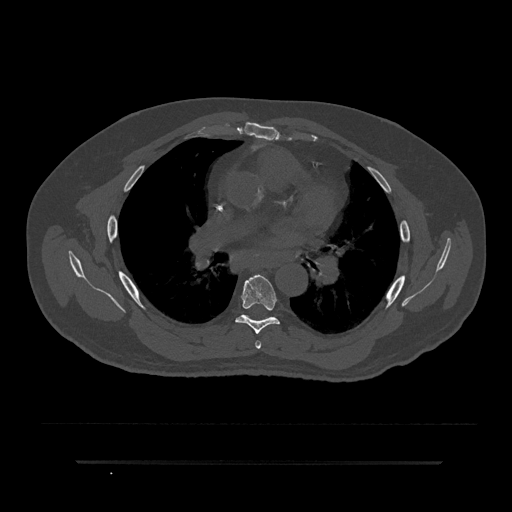
CT including the spine, one axial slice; slice 527 of 797 in the series (ordered by position); reconstruction kernel Br40s/3; 120 kVp; bone window (W 1800 / L 400 HU); 512 × 512 image matrix. Male patient, age 59 years. Case-level facts recorded for this patient, not image findings: primary cancer: bile ducts; vertebrae with lytic lesions (as recorded): T10.
Outlined on this slice (semi-automatically segmented with operator editing):
- T5 vertebra: bounding box [x1, y1, x2, y2] px = [255, 341, 261, 349]
- T6 vertebra: [235, 274, 280, 334]